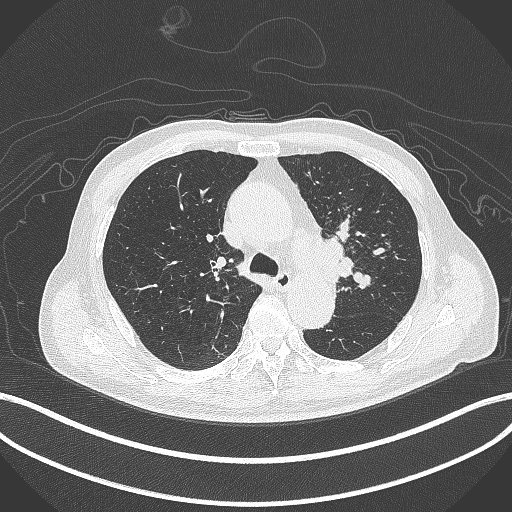
Chest CT, one axial slice; position 298 of 417 along the scan axis; reconstruction kernel B70f; lung window (W 1500 / L -600 HU); 1 mm slice thickness; 512 × 512 image matrix, field of view 400 × 400 mm. Patient: male, 77 years. Case-level facts recorded for this patient, not image findings: clinical TNM (as recorded): T3 N1 M0.
Outlined on this slice (rectangle marked by the reading radiologist):
- lung tumour (recorded histology: adenocarcinoma): bounding box <320,234,359,287> (left, top, right, bottom; pixels)